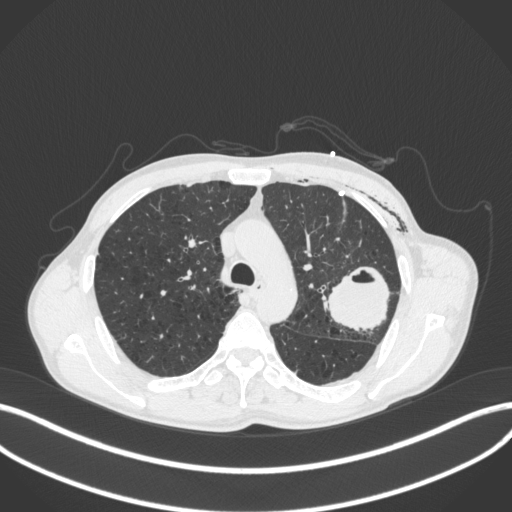
Chest CT, one axial slice; reconstruction kernel B31f; 120 kVp; lung window (W 1500 / L -600 HU); 1 mm slice thickness; 512 × 512 image matrix. Male patient, age 58 years. From the clinical record (not read from this slice): clinical TNM (as recorded): T3 N0 M0.
Structures marked on this image (bounding box drawn by a radiologist):
- lung tumour (recorded histology: adenocarcinoma): bounding box <322,257,391,334> (left, top, right, bottom; pixels)